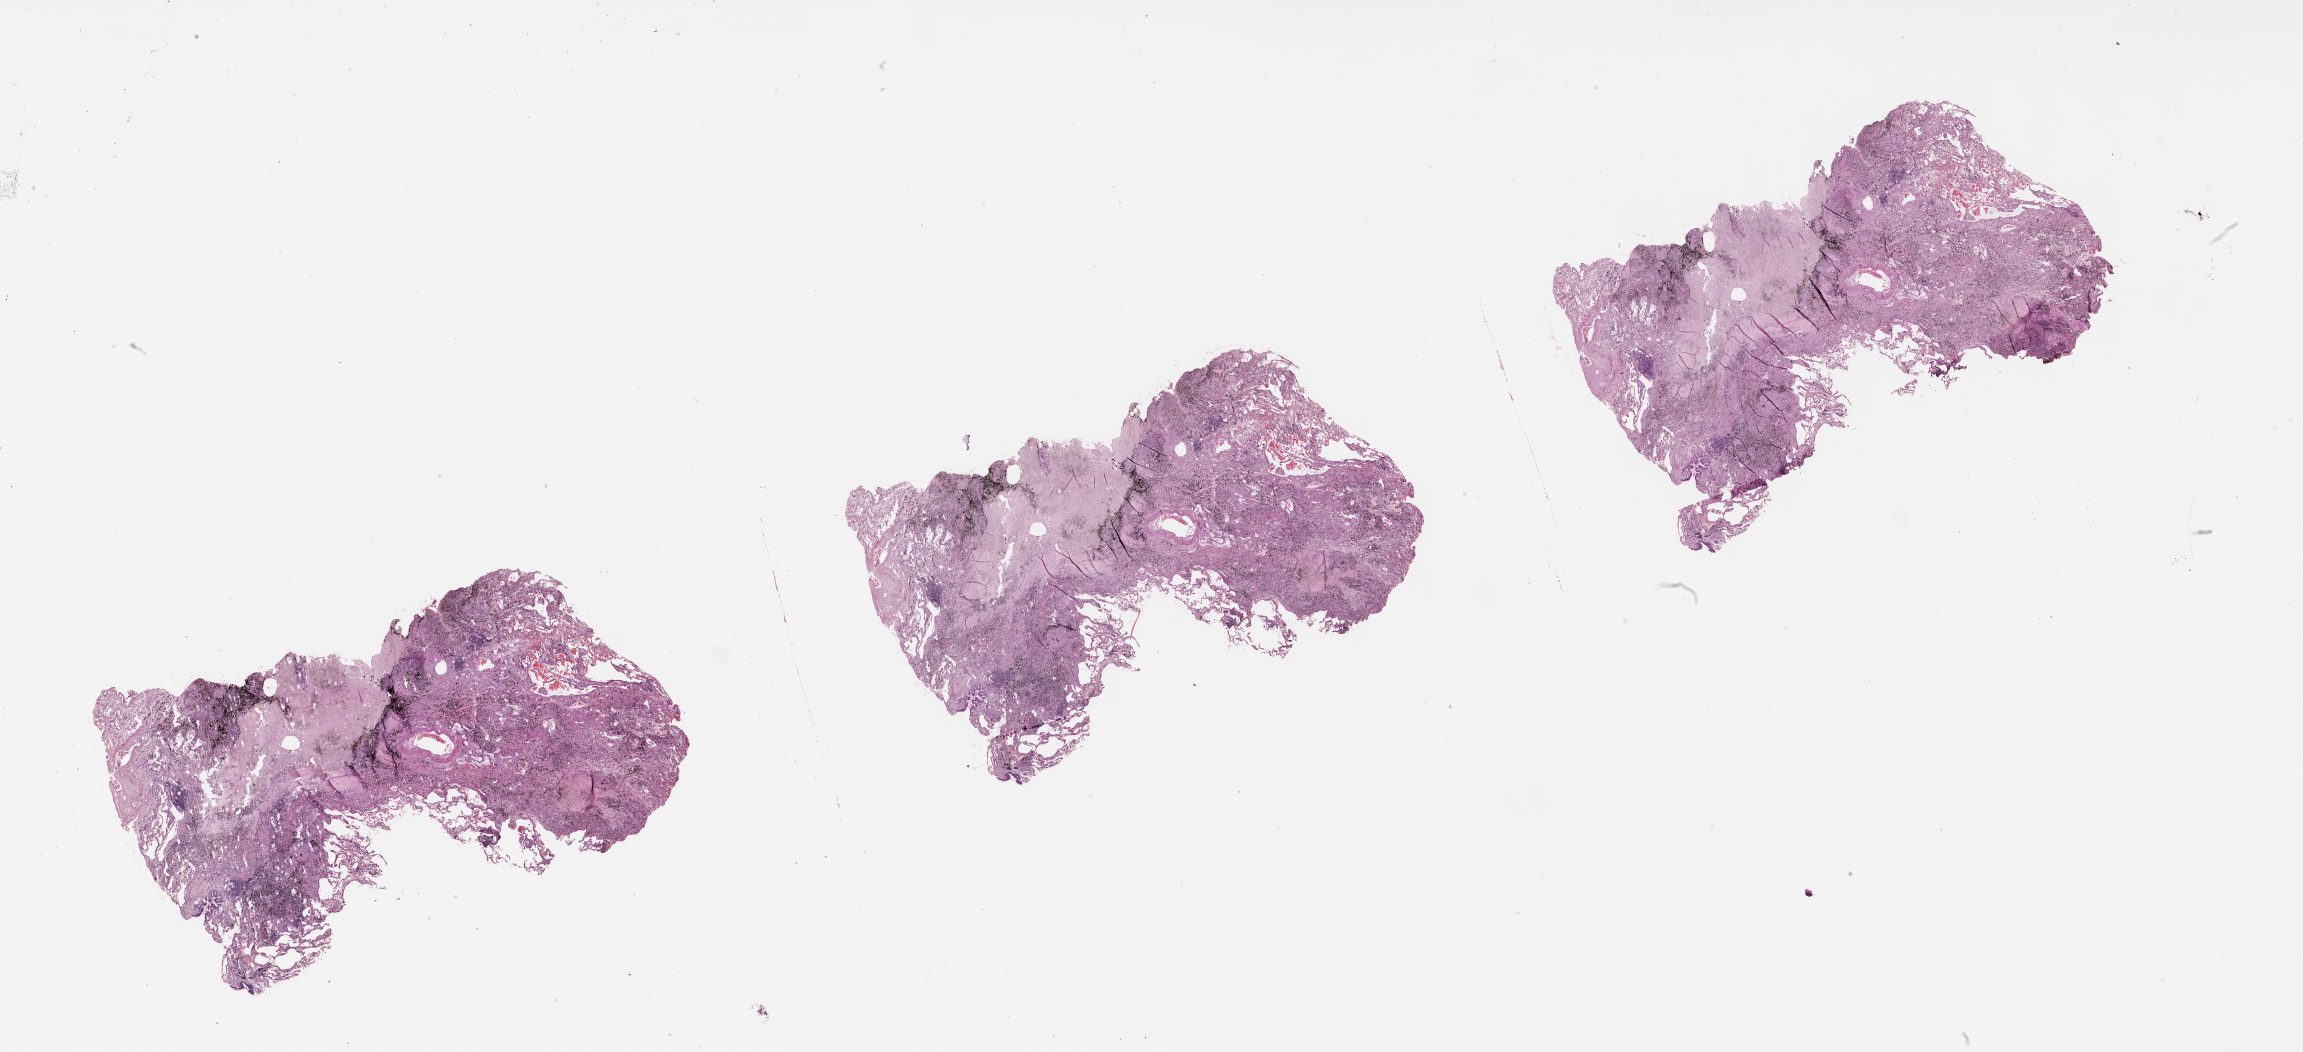
Digitized Hematoxylin and eosin (H&E) stained tissue section (whole slide), low-resolution overview of the scanned area, about 37.1 x 16.9 mm (from a 20x scan). Lung, normal (non-tumour) tissue. Male, 68 y/o.
This section: normal (non-tumour) tissue from the same patient. Patient diagnosis (cohort enrolment): squamous cell carcinoma (lung).